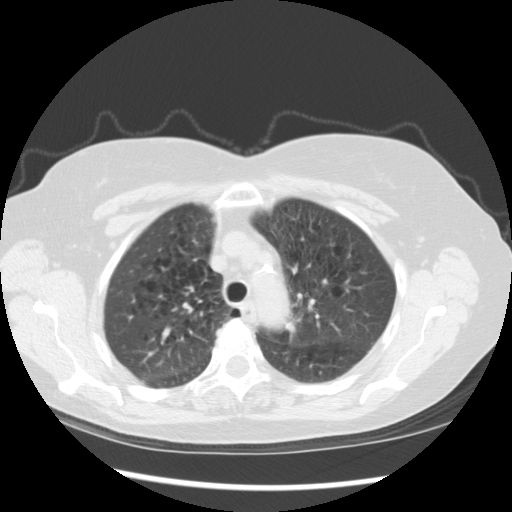
Axial slice from a low-dose chest CT screening exam. Baseline screening round. Lung window (W 1500 / L -600 HU). Standard (soft-tissue) reconstruction kernel (STANDARD). 120 kVp. Female, age 70 years at enrolment. Current smoker at enrolment.
Expert-annotated lung lesion, bounding box [x1, y1, x2, y2] px = [271, 303, 316, 350]. Screening reader's record for this exam: no non-calcified nodule ≥4 mm recorded. Lung cancer was diagnosed 757 days after this screen: neoplasm, malignant, left upper lobe, stage IIIB (AJCC 6th edition), 40 mm at pathology.